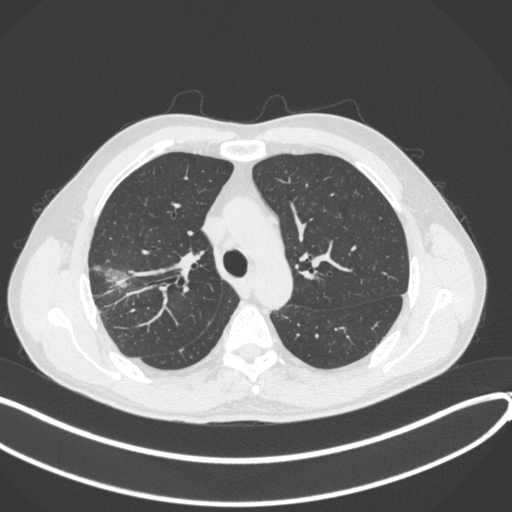
Chest CT, one axial slice; position 298 of 381 along the scan axis; reconstruction kernel B31f; lung window (W 1500 / L -600 HU); 1 mm slice thickness; 512 × 512 image matrix, field of view 400 × 400 mm. Patient: male, 62 years. Case-level facts recorded for this patient, not image findings: clinical TNM (as recorded): T1c N0 M0; histopathological grade: G2-3.
Outlined on this slice (rectangle marked by the reading radiologist):
- lung tumour (recorded histology: adenocarcinoma): box from (x=102, y=267) to (x=133, y=295) px